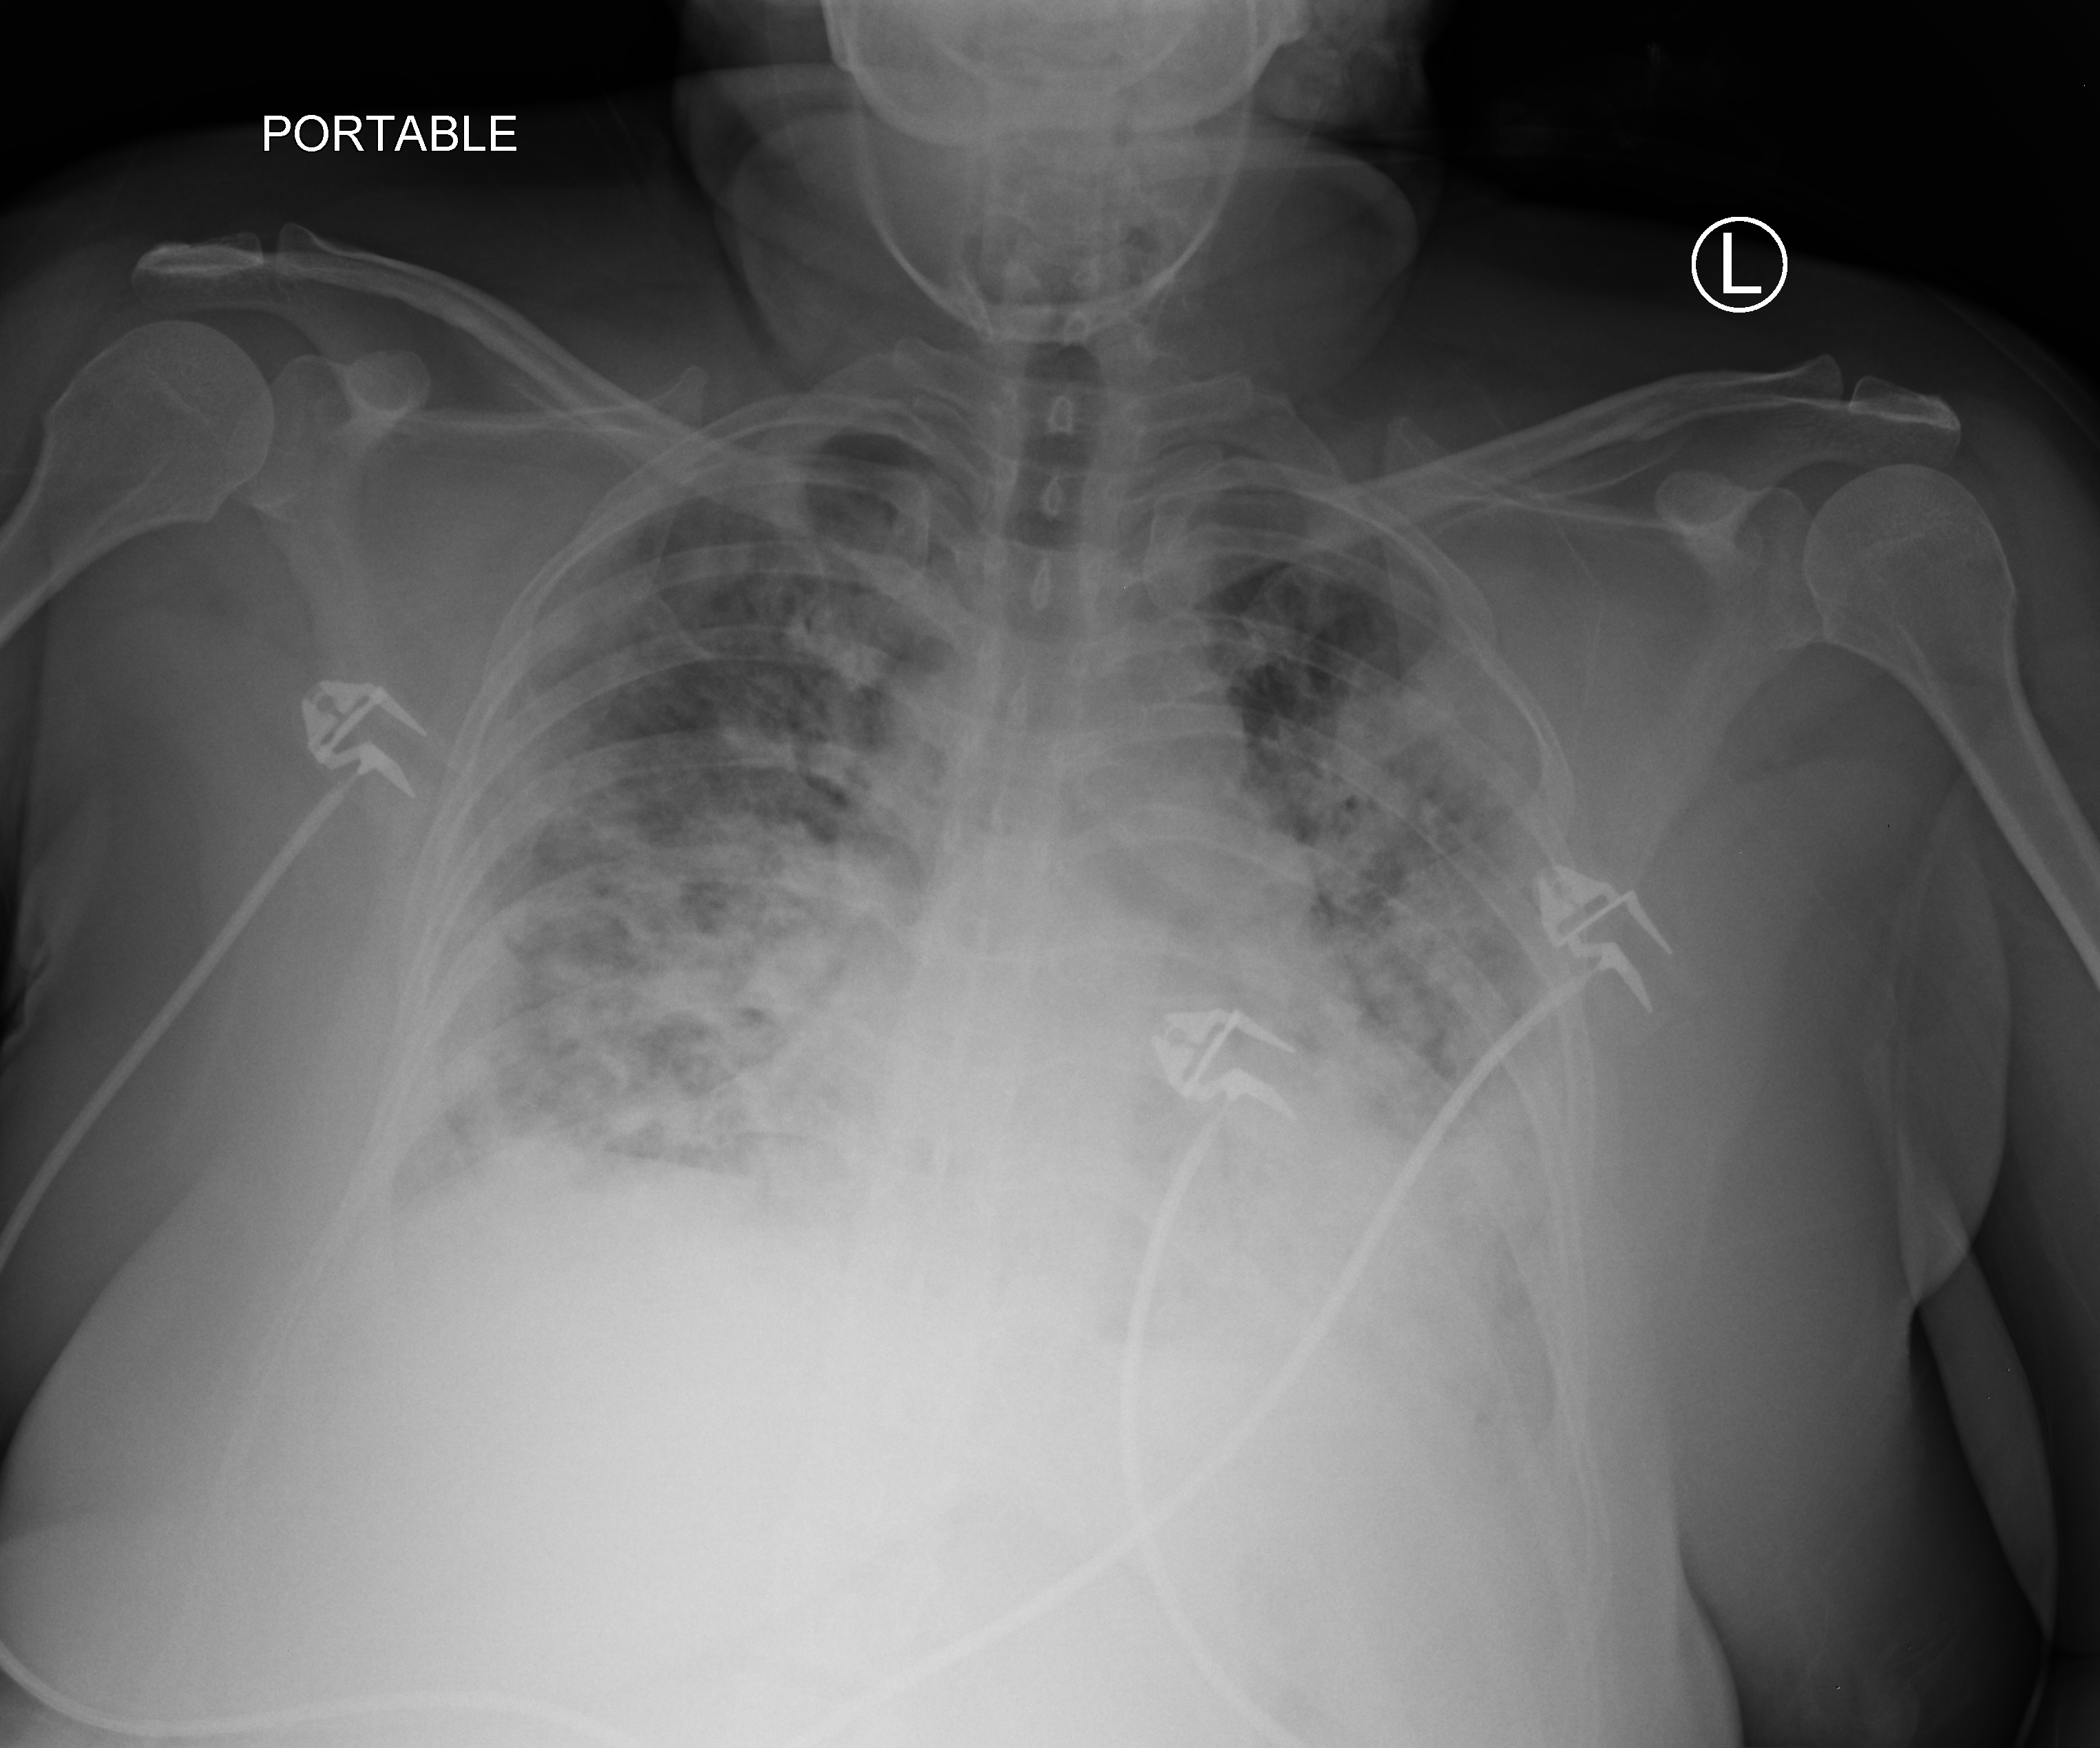
Portable chest radiograph, anteroposterior (AP) projection. Patient hospitalised with COVID-19, aged 18–59 years.
Hospital-stay facts (about this admission, not read from this image; timing relative to this image not recorded): other chronic lung disease (admission record): yes; length of hospital stay: 10 days; admitted to intensive care during this hospital stay: yes.